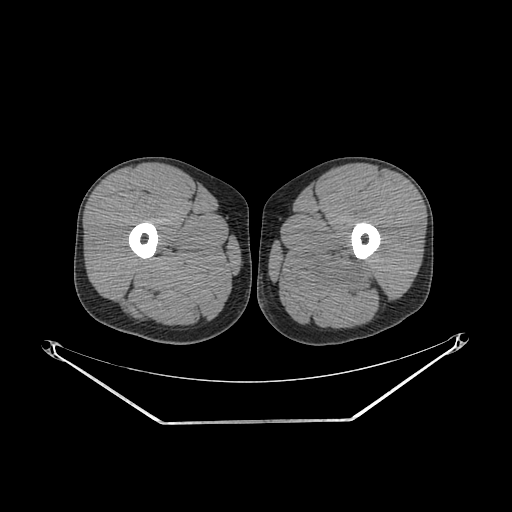
CT of an extremity soft-tissue mass (from a PET/CT study), one axial slice; soft-tissue window (W 400 / L 40 HU); 3.75 mm slice thickness; 512 × 512 image matrix, field of view 500 × 500 mm. Male patient. From the clinical record (not read from this slice): histological type: extraskeletal osteosarcoma; grade: high; site of the primary tumour: left adductur.
Structures marked on this image (expert contour drawn on MRI and transferred to this co-registered scan by the dataset authors):
- gross tumour volume (mass): bounding box <283,244,380,298> (left, top, right, bottom; pixels)